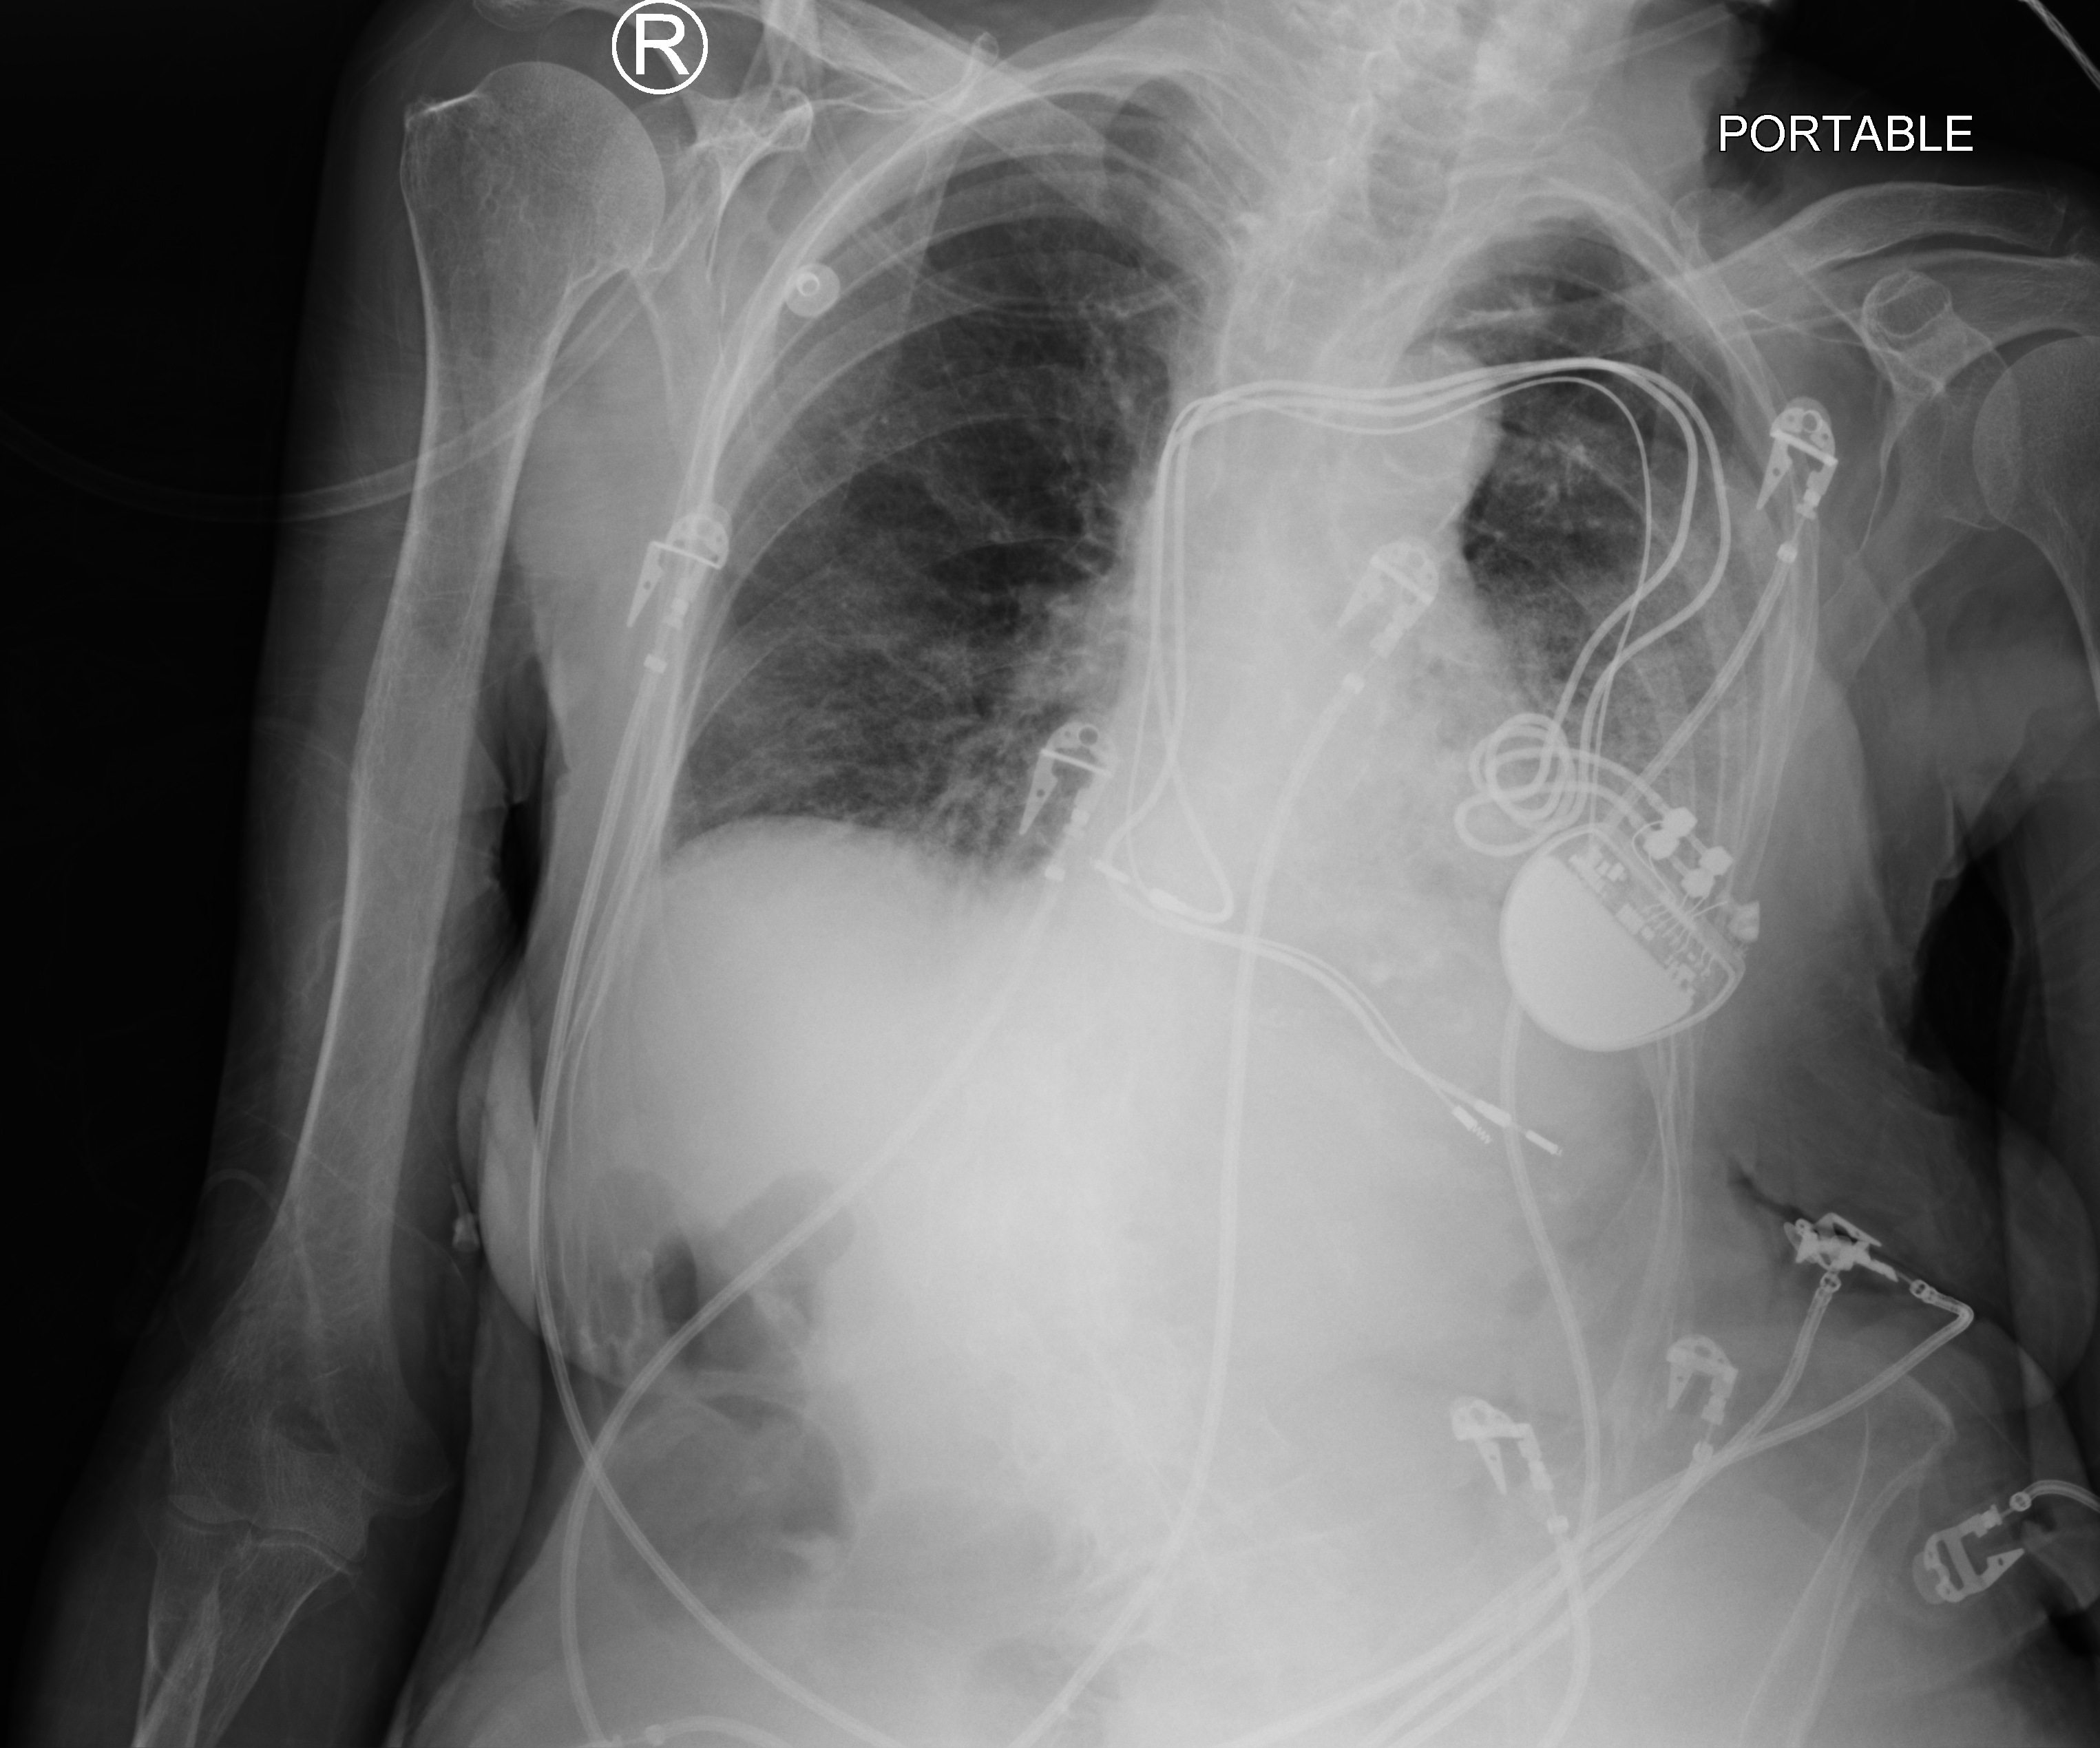
Bedside chest radiograph (computed radiography); anteroposterior (AP) projection. Patient hospitalised with COVID-19; female, aged 75–90 years.
From the hospital-stay record, not from the radiograph (when in the stay this image was taken is not recorded): admitted to intensive care during this hospital stay: no.